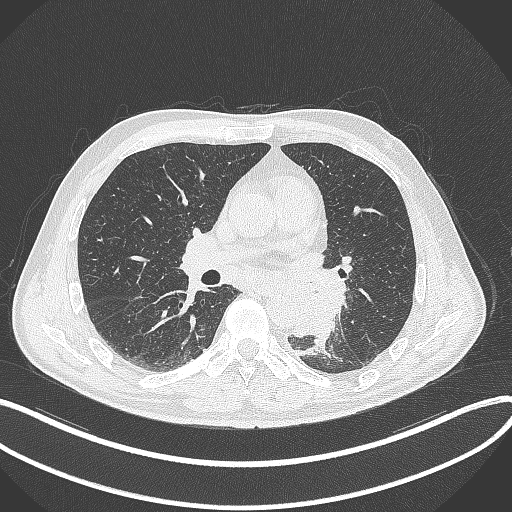
Chest CT, one axial slice; position 176 of 329 along the scan axis; 120 kVp; lung window (W 1500 / L -600 HU); 512 × 512 image matrix, field of view 400 × 400 mm. Patient: male, 59 years. Case-level facts recorded for this patient, not image findings: clinical TNM (as recorded): T2a N2 M0.
Outlined on this slice (rectangle marked by the reading radiologist):
- lung tumour (recorded histology: squamous cell carcinoma): bounding box <264,265,344,337> (left, top, right, bottom; pixels)